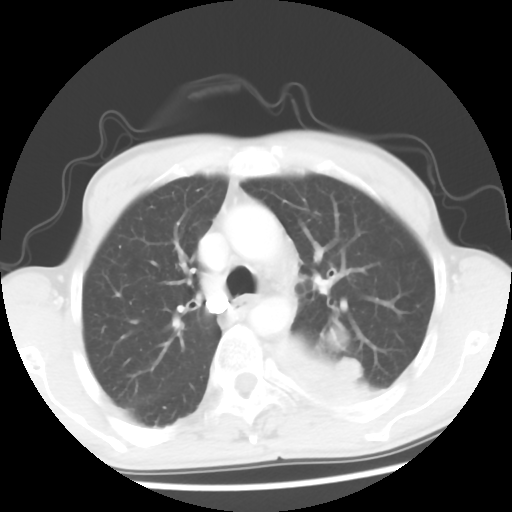
Chest CT, one axial slice. Position 40 of 56 along the scan axis. Lung window (W 1500 / L -600 HU). 5 mm slice thickness. 512 × 512 image matrix, field of view 318 × 318 mm. Male patient, age 60 years. From the clinical record (not read from this slice): clinical TNM (as recorded): T4 N0 M0.
Structures marked on this image (bounding box drawn by a radiologist):
- lung tumour (recorded histology: squamous cell carcinoma): box from (x=265, y=324) to (x=400, y=428) px